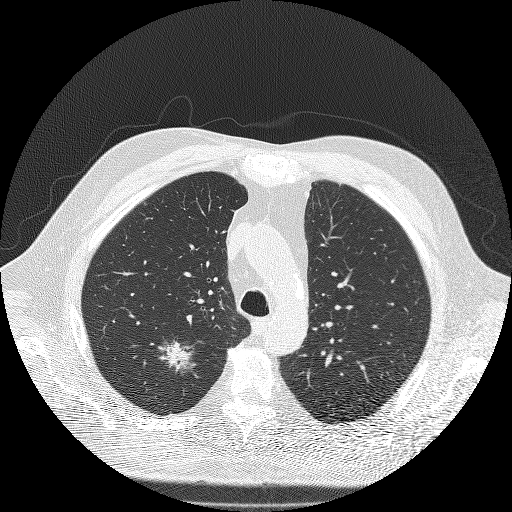
Low-dose screening chest CT, one axial slice; slice 144 of 180 in the series (ordered by position); reconstruction kernel FC51; 120 kVp; lung window (W 1500 / L -600 HU); 2 mm slice thickness; 512 × 512 image matrix.
Outlined on this slice (outlined manually by an expert reader):
- lesion 1 (tumor, upper lobe of right lung): box from (x=158, y=341) to (x=195, y=372) px